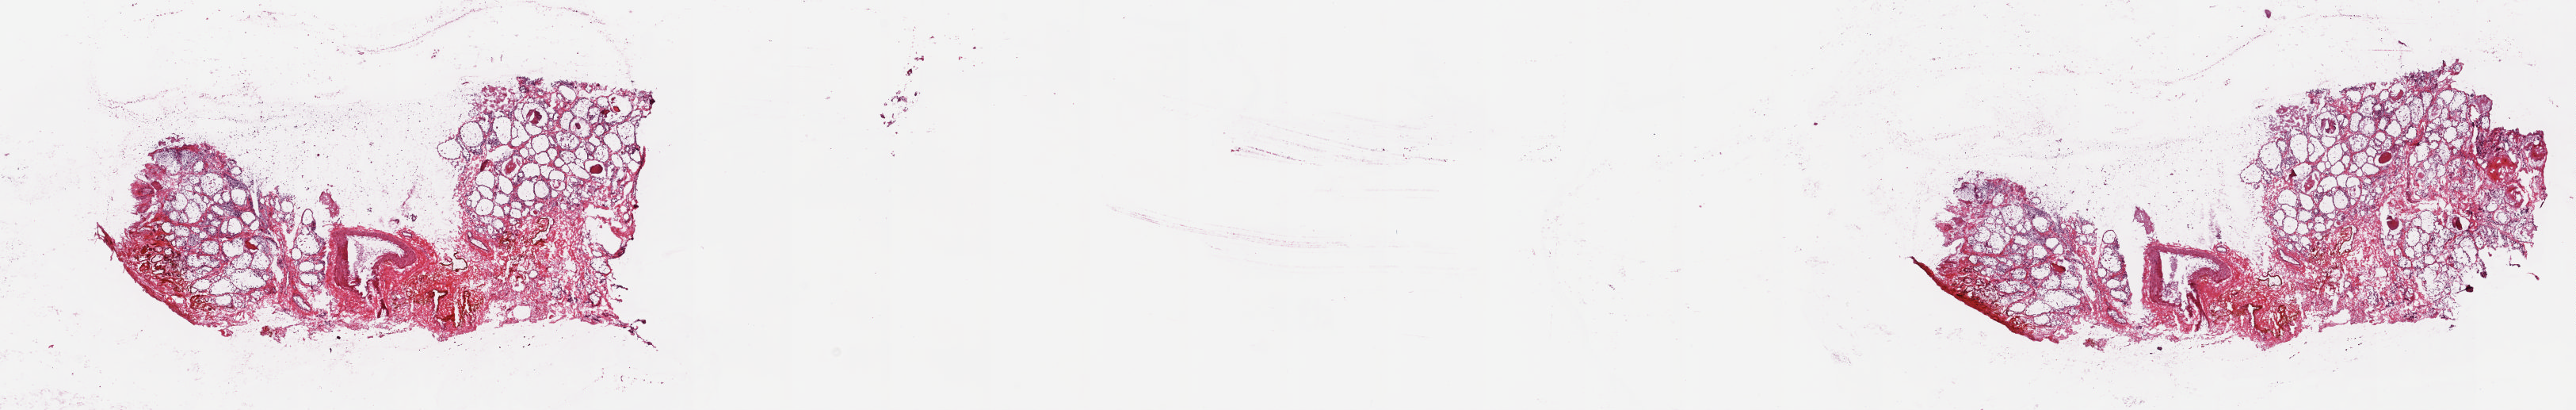
Digitized H&E tissue section (whole slide), whole scanned area (about 25.8 x 4.1 mm) shown as a low-resolution overview. Frozen section from the top of the tissue portion. Thyroid, solid tissue normal (non-tumour tissue) sample. Patient: female, age at initial diagnosis 32 years. Pathologist review of this section (percent, as recorded): tumour cells 0%, tumour nuclei 0%, normal cells 100%, stromal cells 0%, necrosis 0%. Infiltration values recorded for this section: lymphocyte infiltration 0%, monocyte infiltration 0%, neutrophil infiltration 0%.
* this section: solid tissue normal (non-tumour) sample from the same patient
* patient diagnosis: Papillary adenocarcinoma, NOS